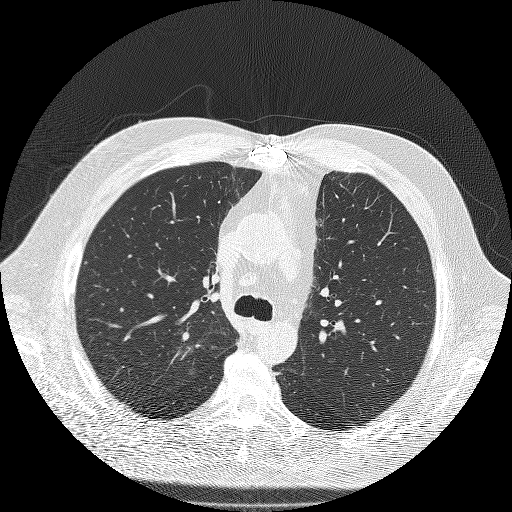
Low-dose screening chest CT, one axial slice; slice 136 of 180 in the series (ordered by position); lung window (W 1500 / L -600 HU); 2 mm slice thickness; 512 × 512 image matrix.
Structures marked on this image (manually delineated by an expert):
- lesion 1 (tumor, upper lobe of right lung): bounding box <182,332,189,342> (left, top, right, bottom; pixels)